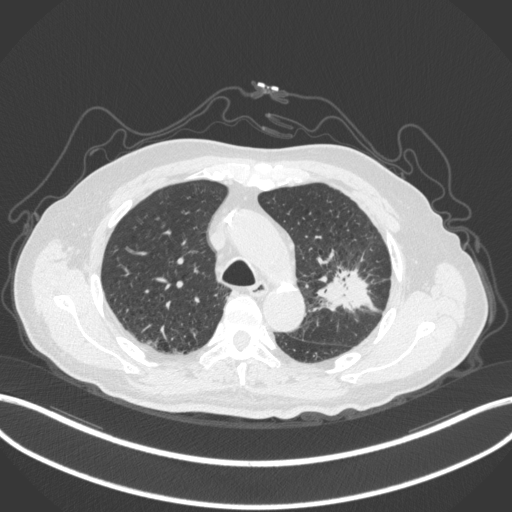
Chest CT, one axial slice; slice 209 of 331 in the series (ordered by position); reconstruction kernel B31f; lung window (W 1500 / L -600 HU); 1 mm slice thickness; 512 × 512 image matrix, field of view 400 × 400 mm. Patient: male, 79 years. From the clinical record (not read from this slice): clinical TNM (as recorded): T2a N1 M1; histopathological grade: G3.
Structures marked on this image (rectangle marked by the reading radiologist):
- lung tumour (recorded histology: adenocarcinoma): box from (x=316, y=264) to (x=376, y=317) px